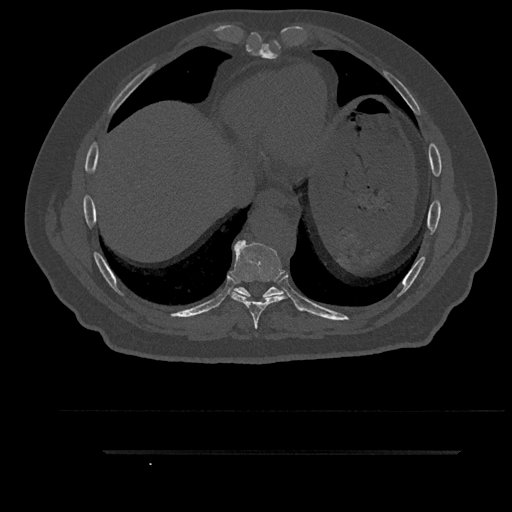
CT including the spine, one axial slice. Position 455 of 797 along the scan axis. Reconstruction kernel Br40s/3. 120 kVp. Bone window (W 1800 / L 400 HU). 0.5 mm slice thickness. 512 × 512 image matrix, field of view 432 × 432 mm. Male patient, age 63 years. From the clinical record (not read from this slice): primary cancer: renal; vertebrae with lytic lesions (as recorded): T8.
Outlined on this slice (semi-automatic segmentation, software-assisted and operator-edited):
- T8 vertebra: bounding box (x1, y1, x2, y2) in pixels: (229, 240, 287, 329)
- T9 vertebra: (232, 286, 284, 298)